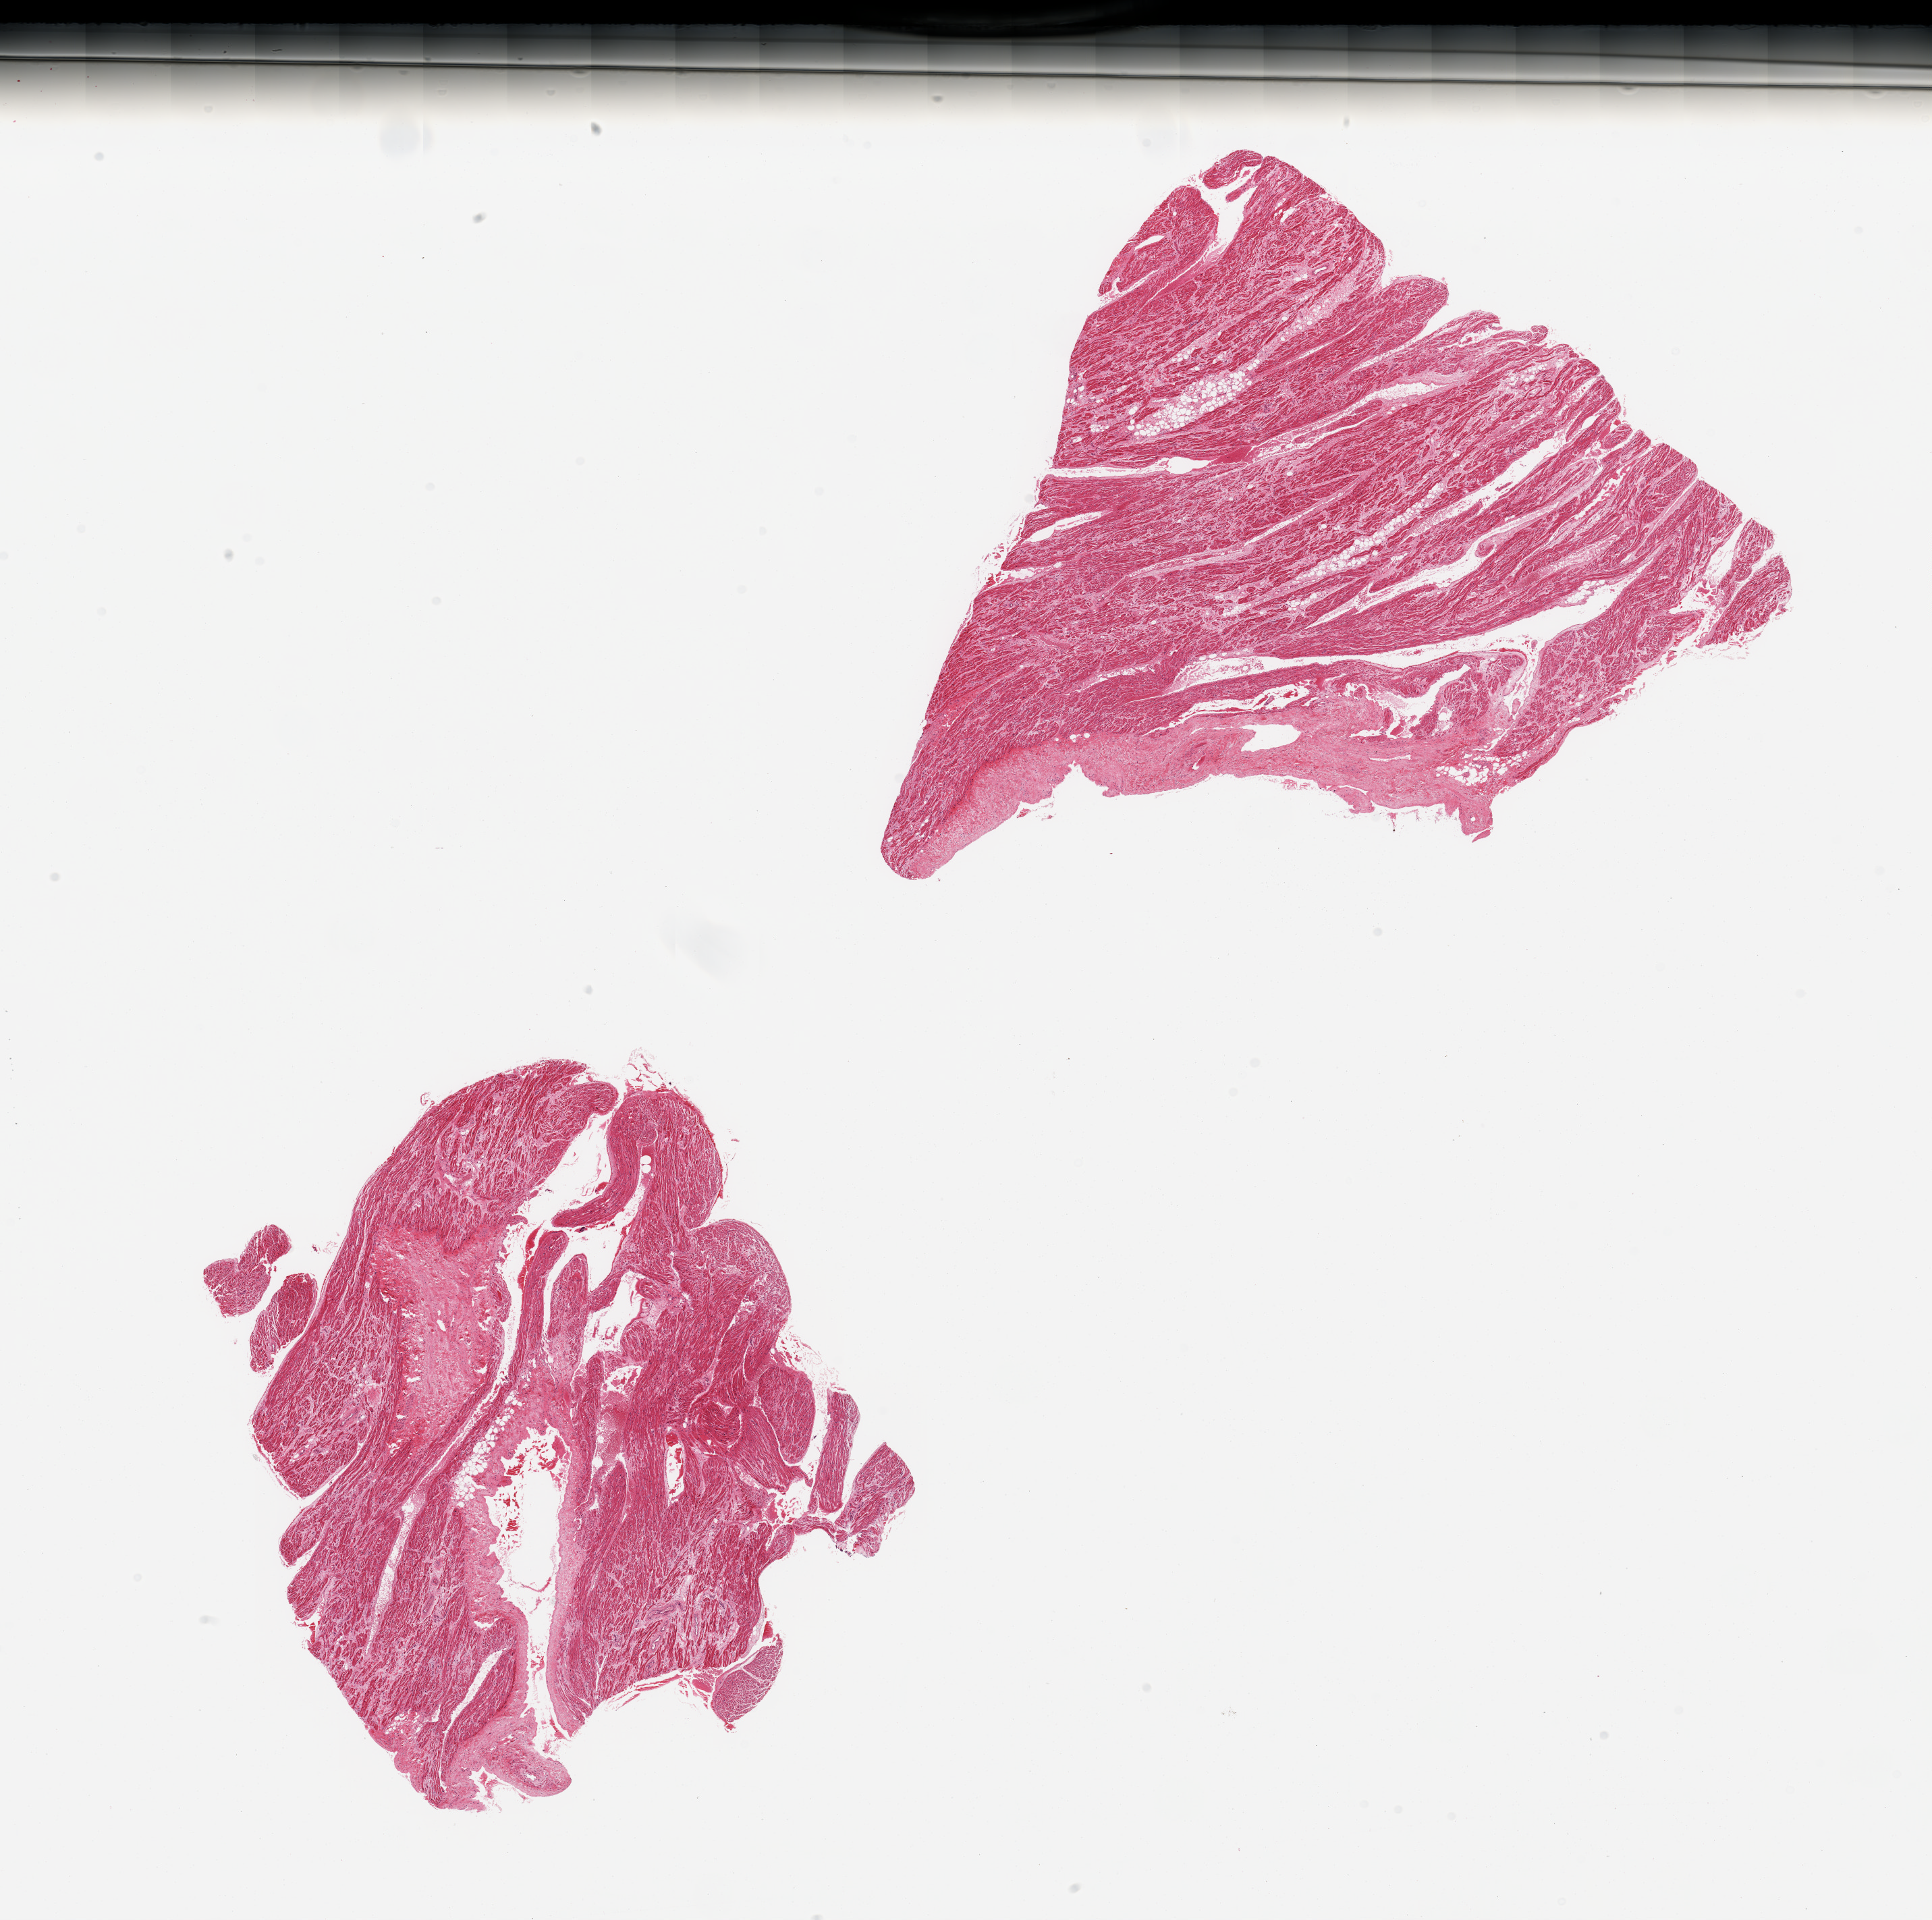
Digitized H&E-stained section — whole scanned area (about 22.6 x 22.5 mm) shown as a low-resolution overview, PAXgene-fixed, paraffin-embedded tissue, sampled site (target tissue): auricular appendage, tissue donor sample. Donor sex: female.
Pathologist's review note for this sample: 2 pieces.